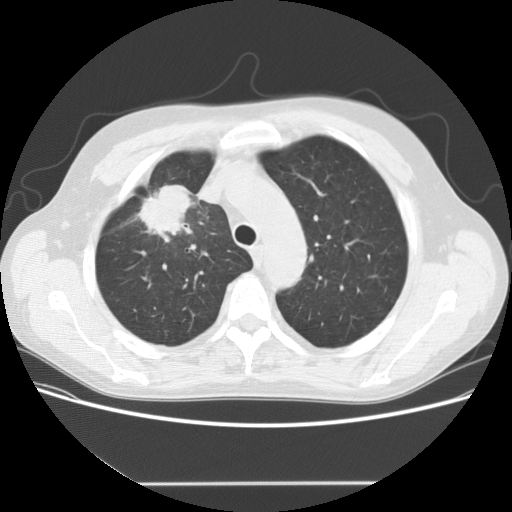
Chest CT (low-dose screening protocol), one axial image; baseline screening round; lung window (W 1500 / L -600 HU); 2.5 mm slice thickness; standard (soft-tissue) reconstruction kernel (STANDARD); slice 35 of 153 in the series. Male, age 56 years at enrolment. Current smoker at enrolment.
Lesion marked by an expert reader, bounding box [x1, y1, x2, y2] px = [128, 173, 211, 243]. The screening reader recorded 2 non-calcified nodules or masses ≥4 mm on this exam; which of them this box marks is not recorded. Official screen result: positive, change unspecified: nodule(s) >= 4 mm or enlarging nodule(s), mass(es), or other non-specific abnormalities suspicious for lung cancer. Lung cancer was diagnosed 120 days after this screen: adenocarcinoma, NOS, right upper lobe, stage IIIA (AJCC 6th edition), 34 mm at pathology.